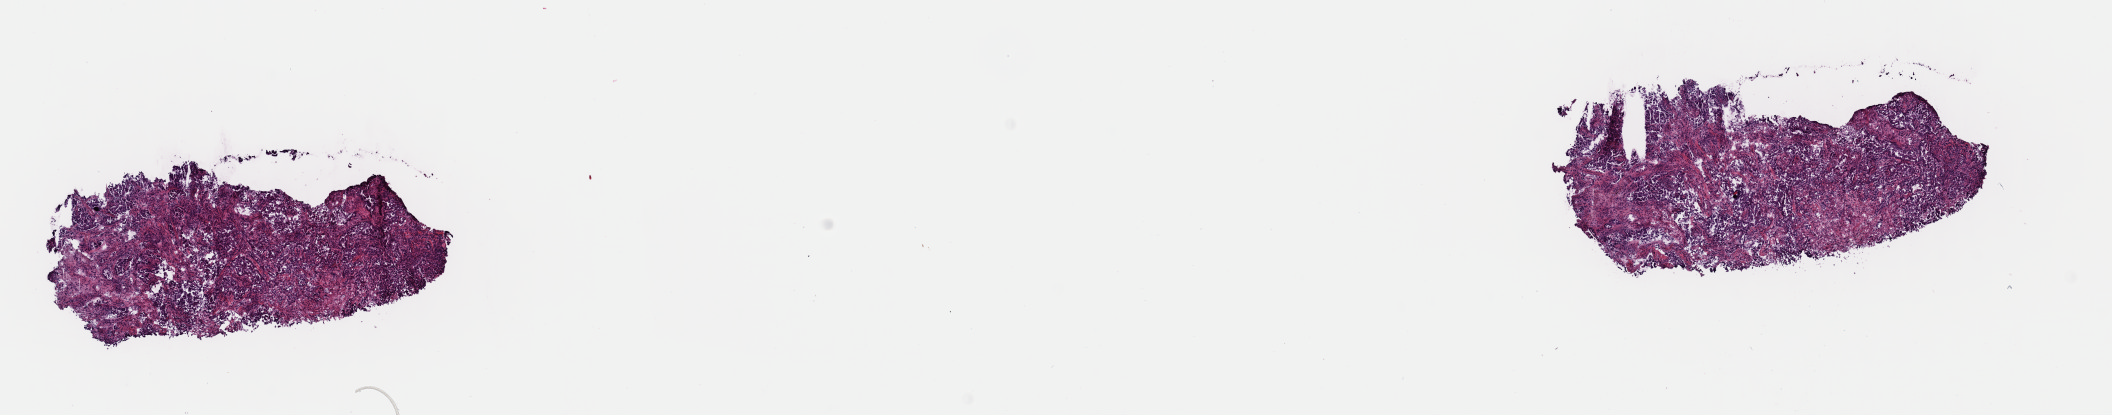
Whole-slide histology image, Hematoxylin and eosin (H&E) stained, low-resolution overview of the scanned area, about 16.7 x 3.3 mm. Frozen section from the top of the tissue portion. Sample: primary tumour, lung. Patient: female, age at initial diagnosis 60 years. Pathologist review of this section (percent, as recorded): tumour cells 45%, tumour nuclei 65%, normal cells 0%, stromal cells 53%, necrosis 2%. Infiltration values recorded for this section: lymphocyte infiltration 10%, monocyte infiltration 2%, neutrophil infiltration 1%.
- AJCC pathologic stage: IA (7th edition)
- TNM: T1a N0 MX
- histologic diagnosis: Adenocarcinoma, NOS (upper lobe, lung)